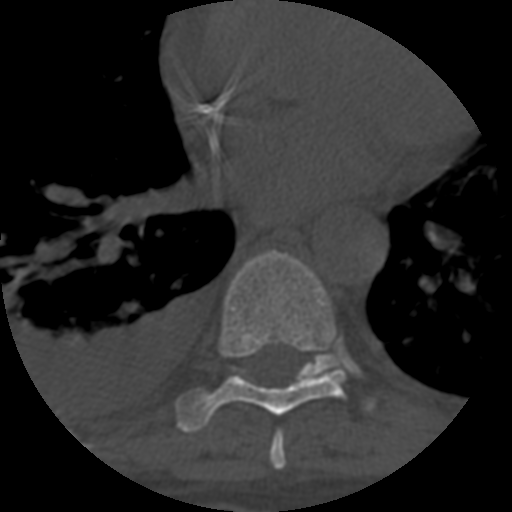
CT including the spine, one axial slice. Position 395 of 708 along the scan axis. 120 kVp. One of 3 acquisitions stored at this slice position. Bone window (W 1800 / L 400 HU). 512 × 512 image matrix. Patient age 55 years. Case-level facts recorded for this patient, not image findings: primary cancer: colon; vertebrae with lytic lesions (as recorded): T12, L1, L5.
Structures marked on this image (semi-automatically segmented with operator editing):
- T7 vertebra: bounding box [x1, y1, x2, y2] px = [270, 433, 286, 467]
- T8 vertebra: [176, 251, 346, 433]
- T9 vertebra: [232, 354, 343, 377]